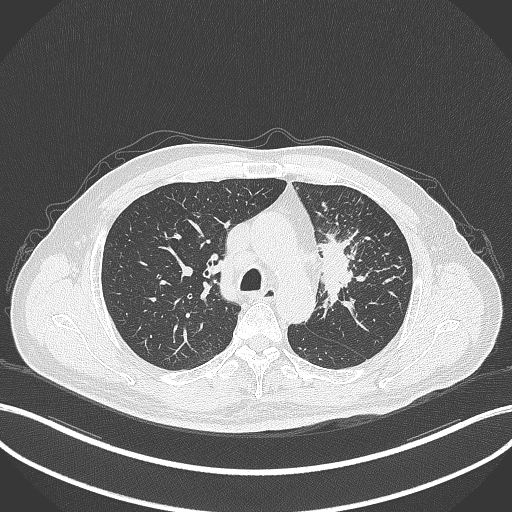
Chest CT, one axial slice. Slice 243 of 386 in the series (ordered by position). Reconstruction kernel B70f. Lung window (W 1500 / L -600 HU). 1 mm slice thickness. 512 × 512 image matrix, field of view 400 × 400 mm. Male patient, age 69 years. From the clinical record (not read from this slice): clinical TNM (as recorded): T2a N2 M0; histopathological grade: G2-3.
Annotated regions visible in this slice (bounding box drawn by a radiologist):
- lung tumour (recorded histology: adenocarcinoma): bounding box <315,231,365,315> (left, top, right, bottom; pixels)